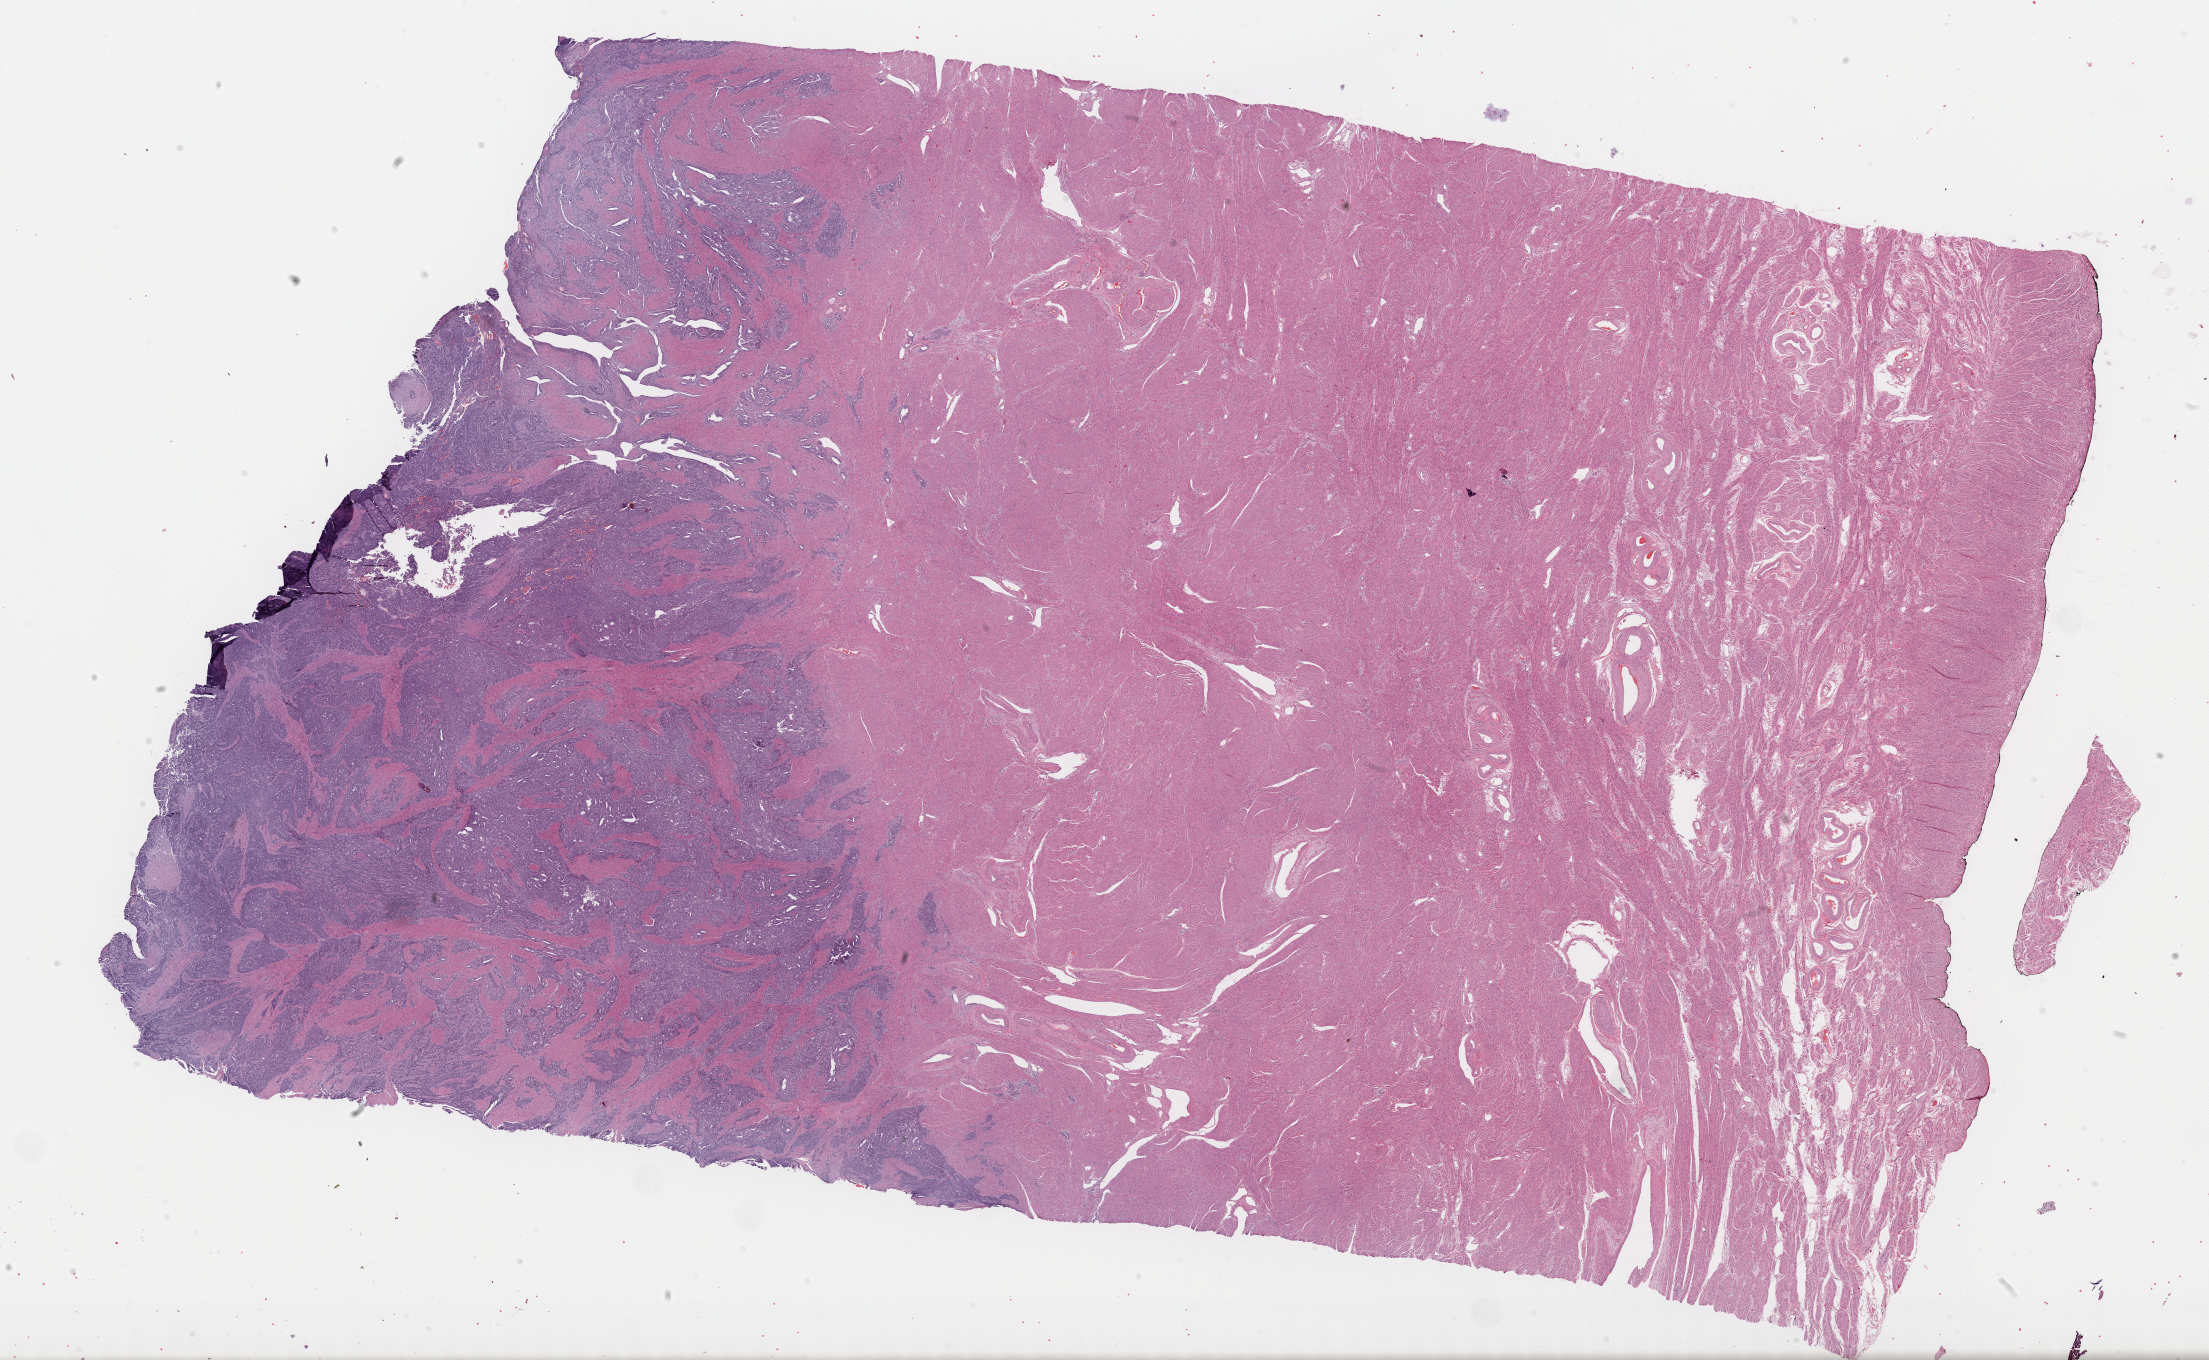
Whole-slide histology image, Hematoxylin and eosin (H&E) stained, whole scanned area (about 35.7 x 22.0 mm) shown as a low-resolution overview. Formalin-fixed paraffin-embedded (FFPE) diagnostic section. Sample: primary tumour, uterus. Female, age 61 years at initial diagnosis. Histologic grade: G3 (poorly differentiated).
* FIGO stage: IB
* diagnosis: Serous cystadenocarcinoma, NOS (endometrium)